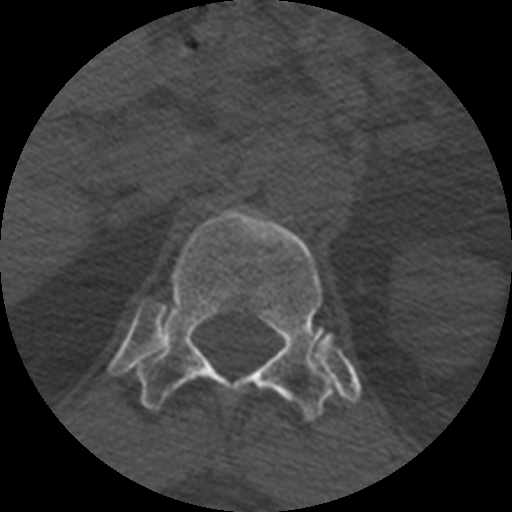
CT including the spine, one axial slice; slice 387 of 399 in the series (ordered by position); reconstruction kernel STANDARD; 120 kVp; bone window (W 1800 / L 400 HU); 1.25 mm slice thickness; 512 × 512 image matrix, field of view 160 × 160 mm. Patient age 71 years. Case-level facts recorded for this patient, not image findings: primary cancer: prostate.
Outlined on this slice (semi-automatic segmentation, software-assisted and operator-edited):
- T12 vertebra: bounding box <135,208,335,422> (left, top, right, bottom; pixels)